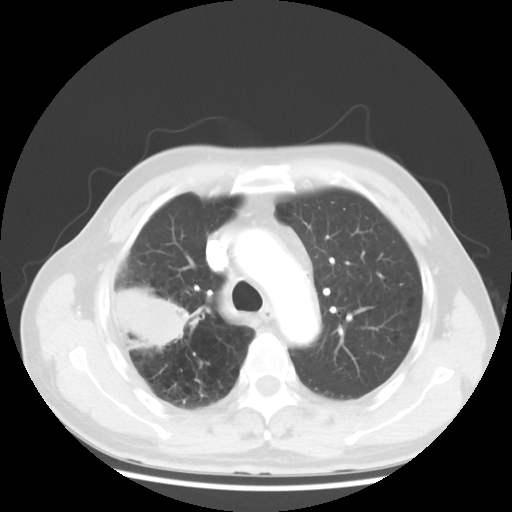
Chest CT, one axial slice. Position 36 of 50 along the scan axis. Lung window (W 1500 / L -600 HU). 5 mm slice thickness. 512 × 512 image matrix, field of view 360 × 360 mm. Patient: male, 69 years. Case-level facts recorded for this patient, not image findings: clinical TNM (as recorded): T3 N0 M0.
Structures marked on this image (bounding box drawn by a radiologist):
- lung tumour (recorded histology: adenocarcinoma): box from (x=109, y=281) to (x=195, y=352) px